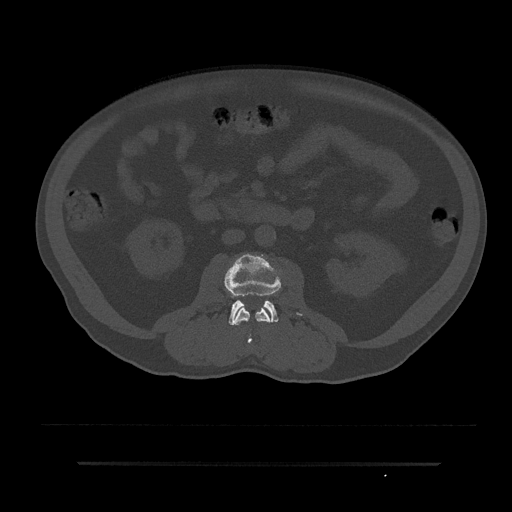
CT including the spine, one axial slice; slice 34 of 797 in the series (ordered by position); reconstruction kernel Br40s/3; 120 kVp; bone window (W 1800 / L 400 HU); 0.5 mm slice thickness; 512 × 512 image matrix, field of view 464 × 464 mm. Male patient, age 59 years. From the clinical record (not read from this slice): primary cancer: bile ducts.
Outlined on this slice (semi-automatic segmentation, software-assisted and operator-edited):
- L2 vertebra: bounding box <233,304,273,344> (left, top, right, bottom; pixels)
- L3 vertebra: <225,255,280,325>